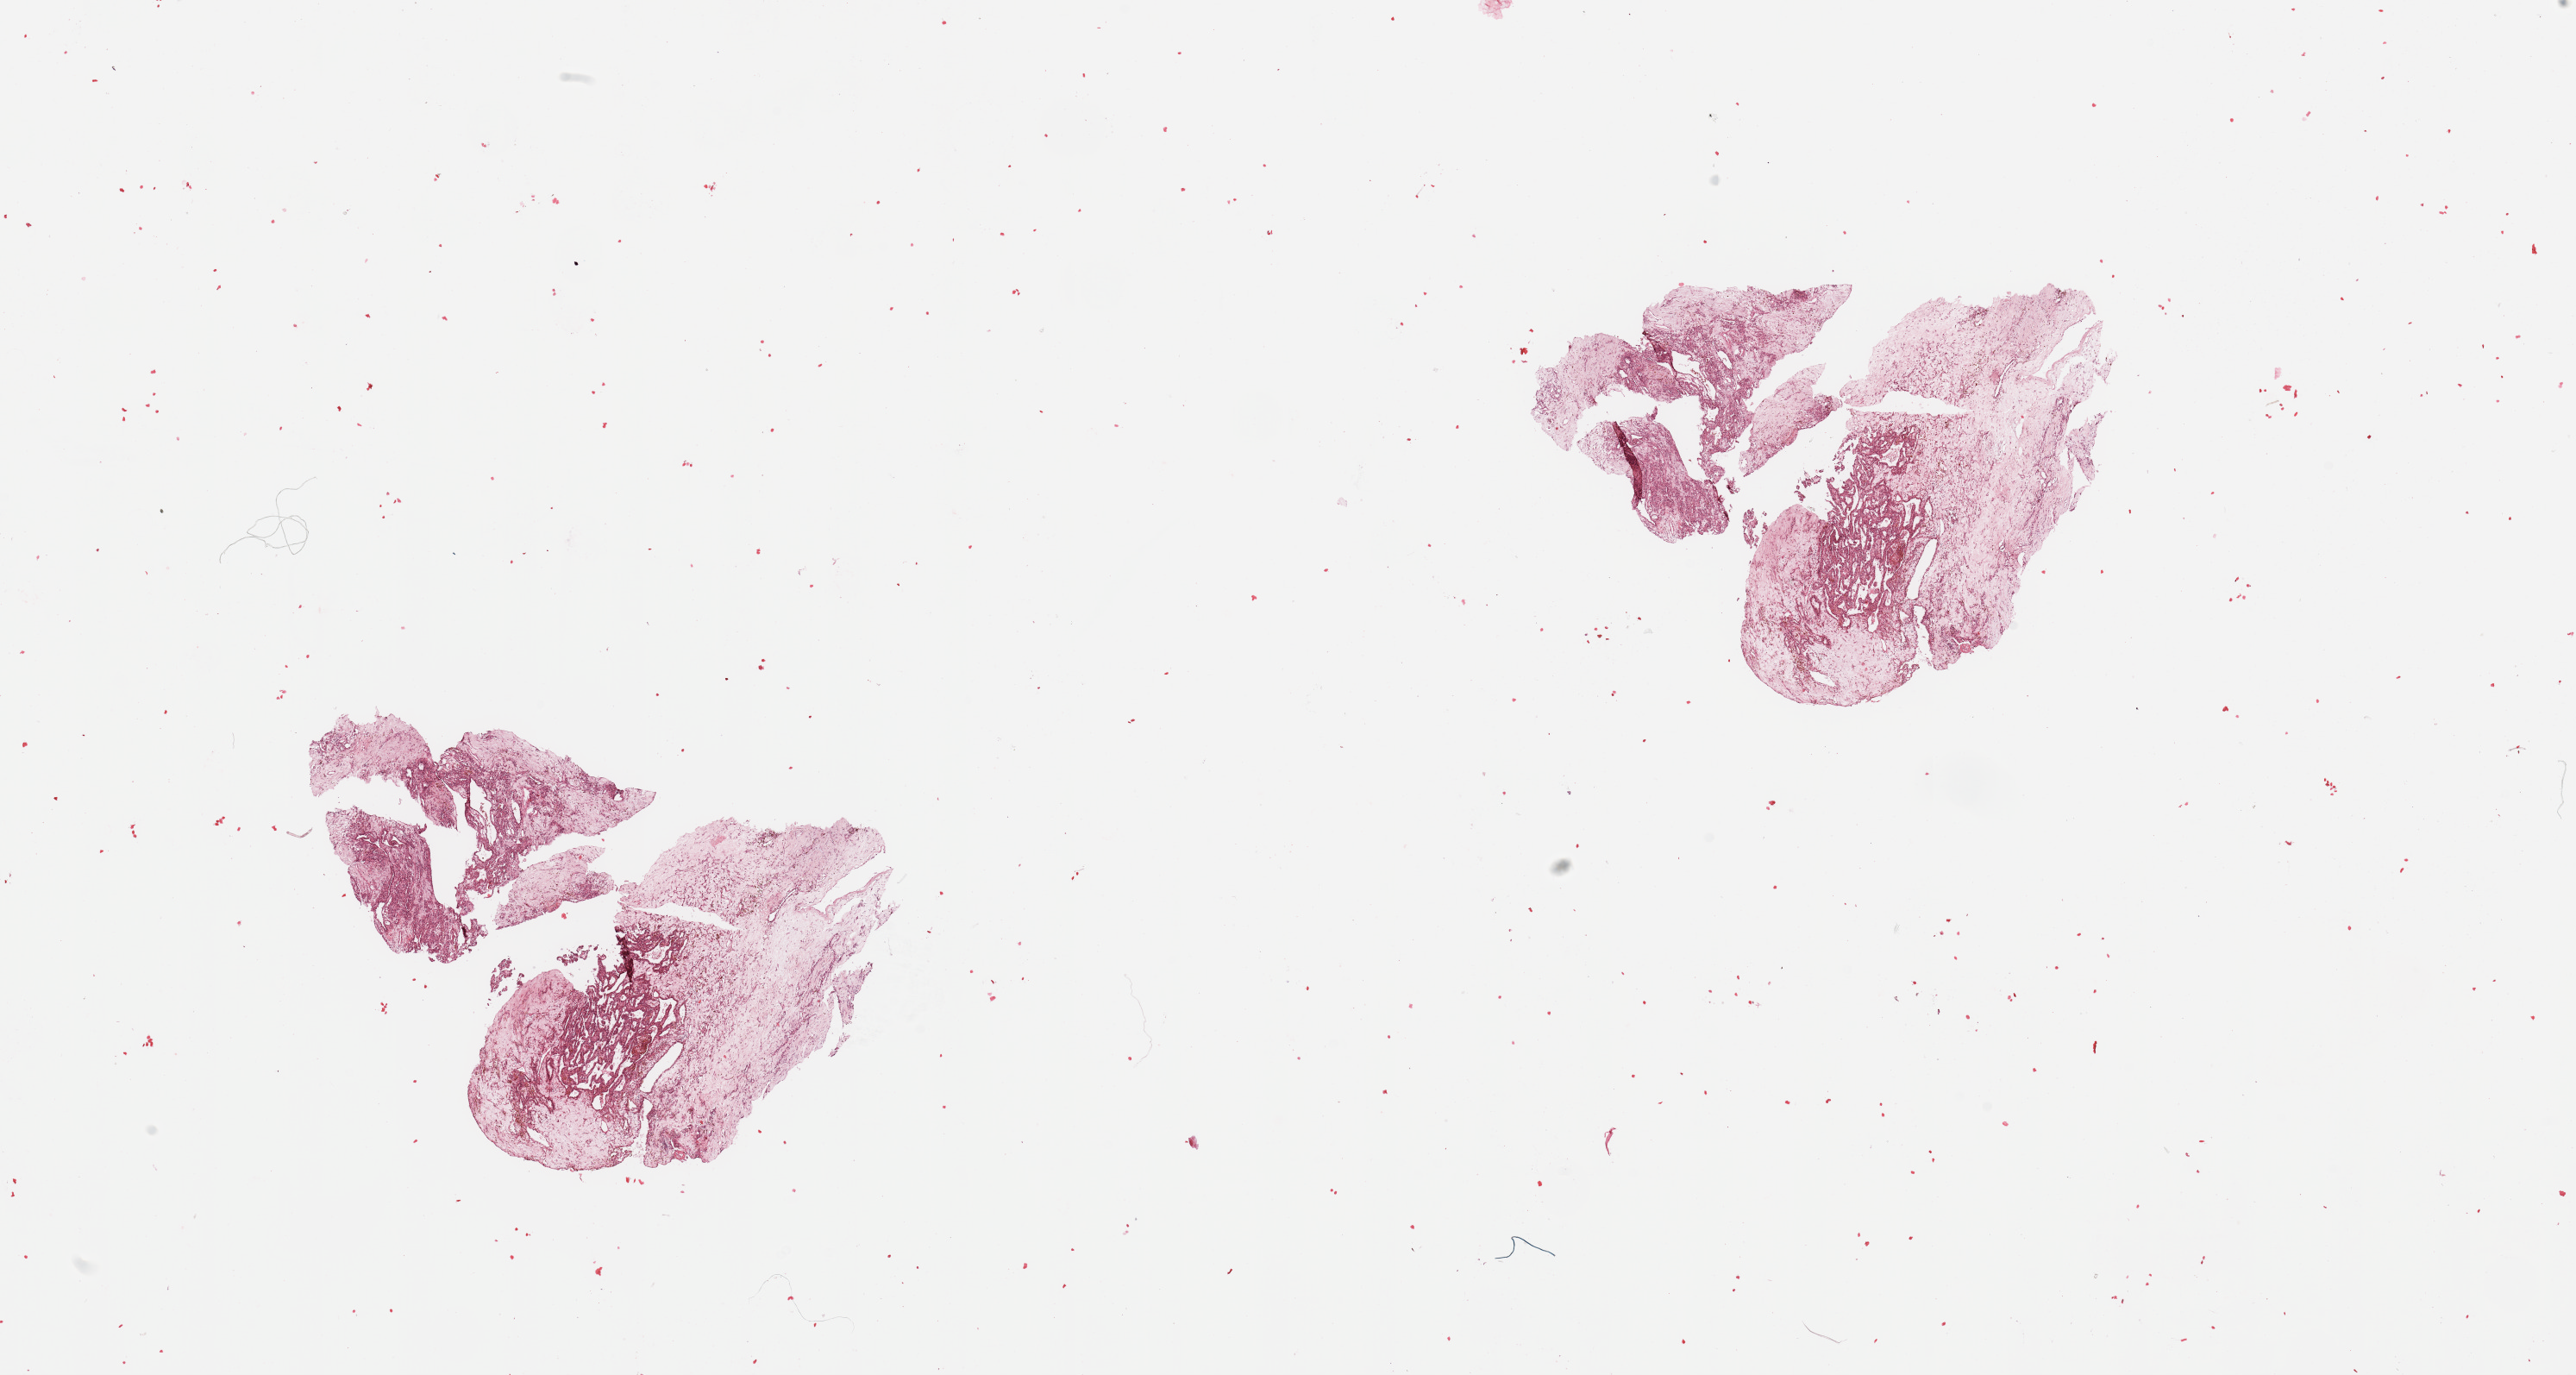
Whole-slide histology image, H&E-stained — shown as a low-resolution overview of the whole scanned area (about 23.6 x 12.6 mm); tumour tissue sample, kidney. Male, 67 y/o.
Diagnosis: Renal cell carcinoma, NOS.